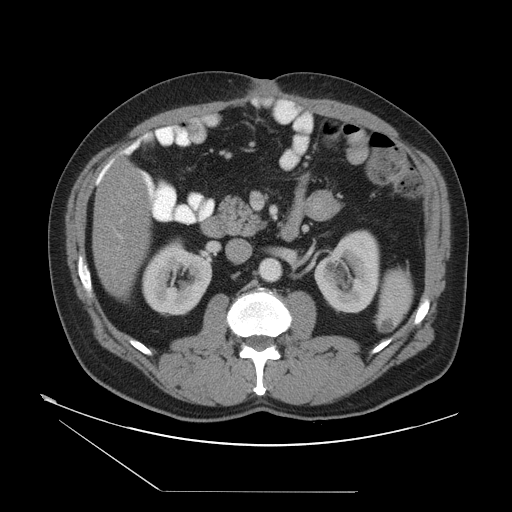
Contrast-enhanced abdominal CT, one axial slice; position 18 of 55 along the scan axis; reconstruction kernel STANDARD; soft-tissue window (W 400 / L 40 HU); 5 mm slice thickness; 512 × 512 image matrix, field of view 454 × 454 mm. Male patient, age 59 years. Case-level facts recorded for this patient, not image findings: diagnosis: colorectal cancer liver metastases, imaged before liver resection; multiple liver metastases: yes; largest metastasis: 0.3 cm; disease in both lobes: yes.
Annotated regions visible in this slice (manually delineated by an expert):
- hepatic veins: bounding box <120,218,124,223> (left, top, right, bottom; pixels)
- liver: <93,162,149,298>
- planned liver remnant (the part of the liver to remain after resection): <93,162,149,298>
- portal vein (with intrahepatic branches): <112,201,125,240>